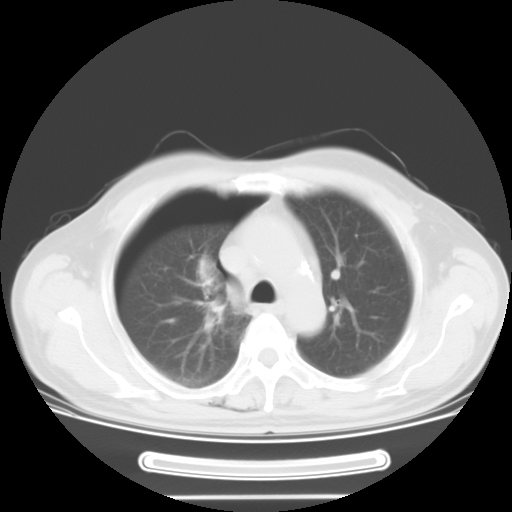
Chest CT, one axial slice; slice 21 of 29 in the series (ordered by position); reconstruction kernel STANDARD; 120 kVp; lung window (W 1500 / L -600 HU); 512 × 512 image matrix, field of view 376 × 376 mm. Male patient, age 61 years. From the clinical record (not read from this slice): clinical TNM (as recorded): T1c N3 M1b.
Annotated regions visible in this slice (bounding box drawn by a radiologist):
- lung tumour (recorded histology: adenocarcinoma): box from (x=186, y=253) to (x=241, y=347) px